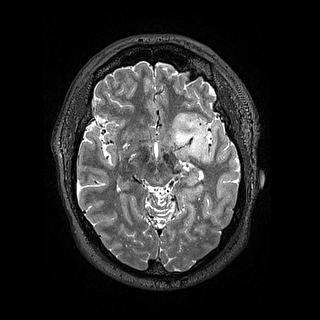
Brain MRI from a brain-tumour surgery series, one axial slice; 1.2 mm slice thickness; 320 × 320 image matrix, field of view 254 × 254 mm. Case-level facts recorded for this patient, not image findings: histopathology: Astrocytoma; WHO grade: 2; IDH mutation: yes; tumour location: Left Insular.
Annotated regions visible in this slice (manually delineated by an expert):
- tumour: bounding box (x1, y1, x2, y2) in pixels: (173, 110, 209, 159)